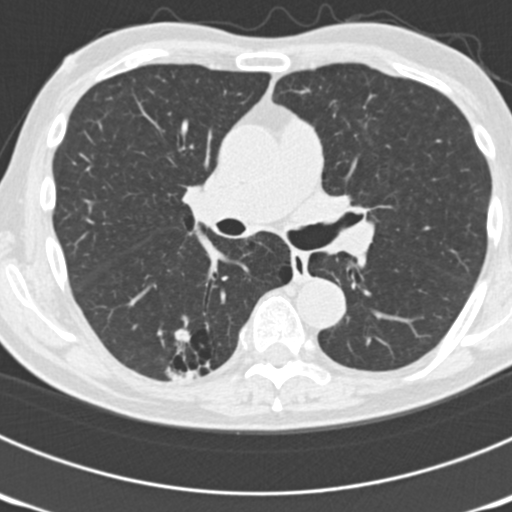
Low-dose screening chest CT, axial slice. Third screening round (two years after baseline). Lung window (W 1500 / L -600 HU). 512 × 512 image matrix, field of view 300 × 300 mm. Male participant, aged 70 years at enrolment.
• Expert reader's lesion annotation, bounding box (x1, y1, x2, y2) in pixels: (144, 309, 237, 386).
• The screening reader recorded 3 non-calcified nodules or masses ≥4 mm on this exam (right upper lobe, left upper lobe, right lower lobe); which of them this box marks is not recorded.
• Lung cancer was diagnosed 14 days after this screen: bronchiolo-alveolar adenocarcinoma, NOS, right lower lobe, poorly differentiated (G3), stage IB (AJCC 6th edition), 30 mm at pathology.